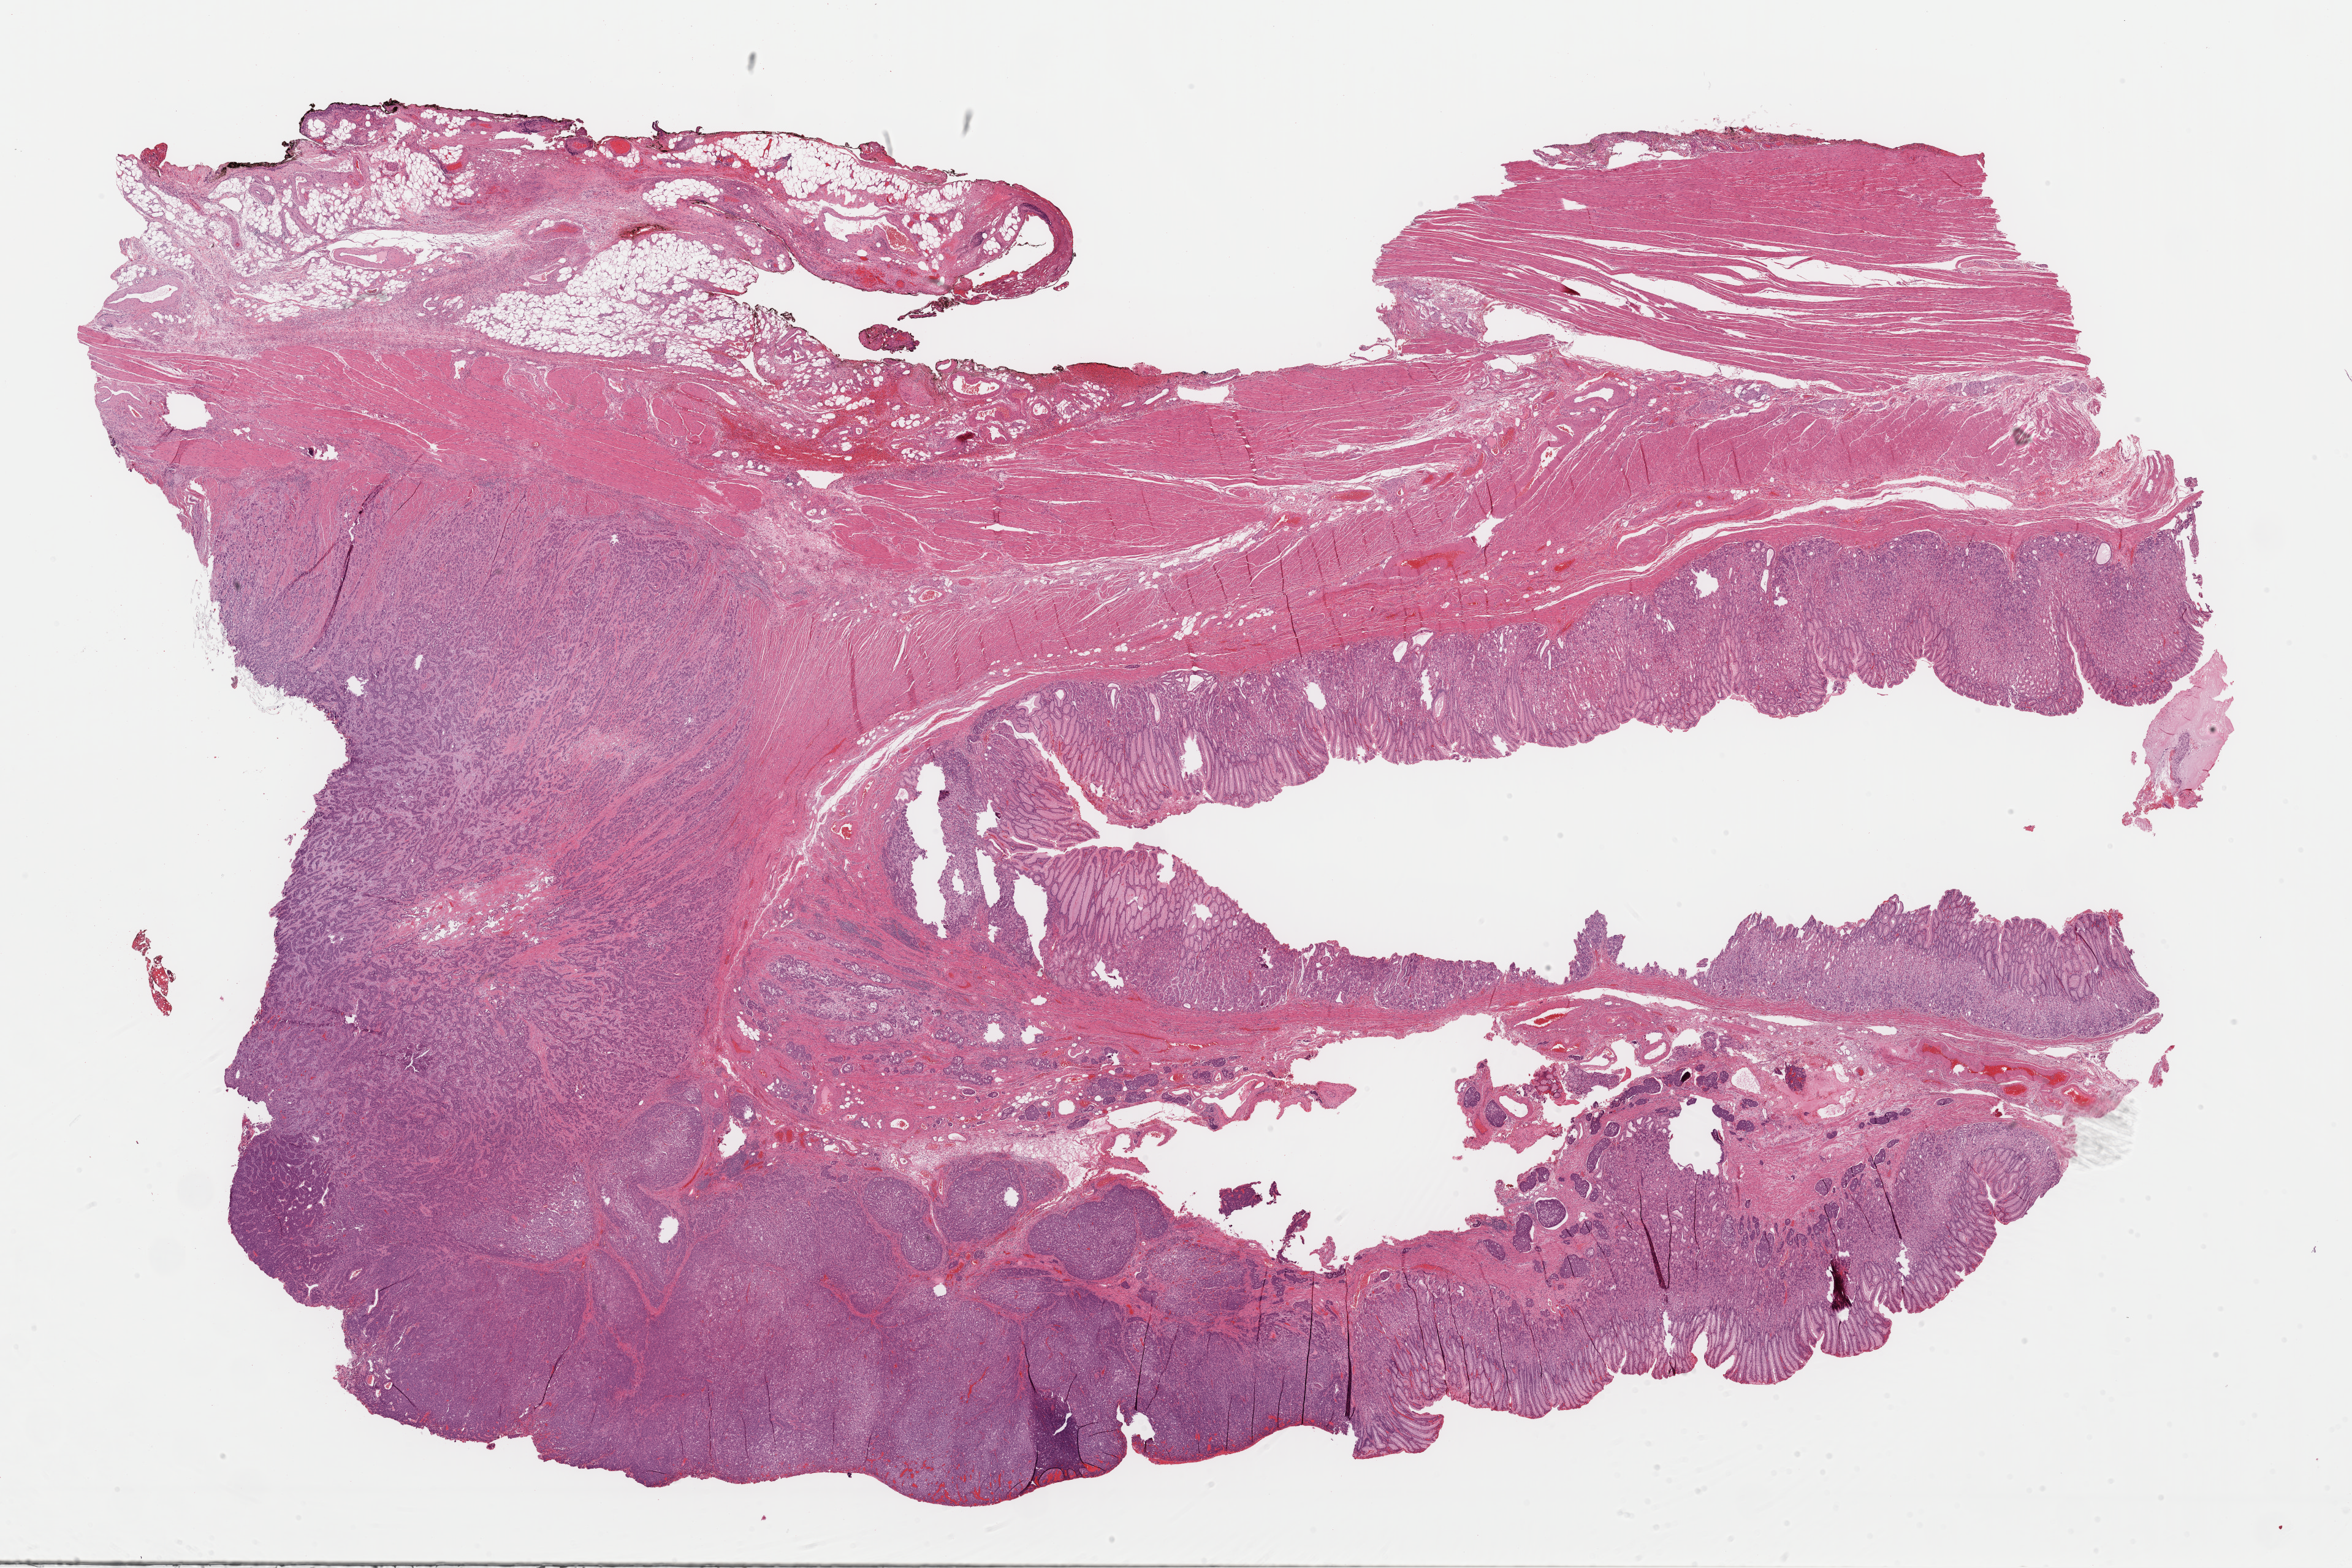
Digitized Hematoxylin and eosin (H&E) stained tissue section (whole slide), a low-resolution overview of the entire scanned area, about 30.3 x 20.2 mm, formalin-fixed paraffin-embedded (FFPE) diagnostic section, sample: primary tumour, stomach. Male patient; age at initial diagnosis 68 years. Histologic grade: G3 (poorly differentiated).
AJCC pathologic stage: IIB (7th edition). Lymph nodes positive (case pathology): 9 of 14 examined. Pathologic diagnosis: Adenocarcinoma, NOS.